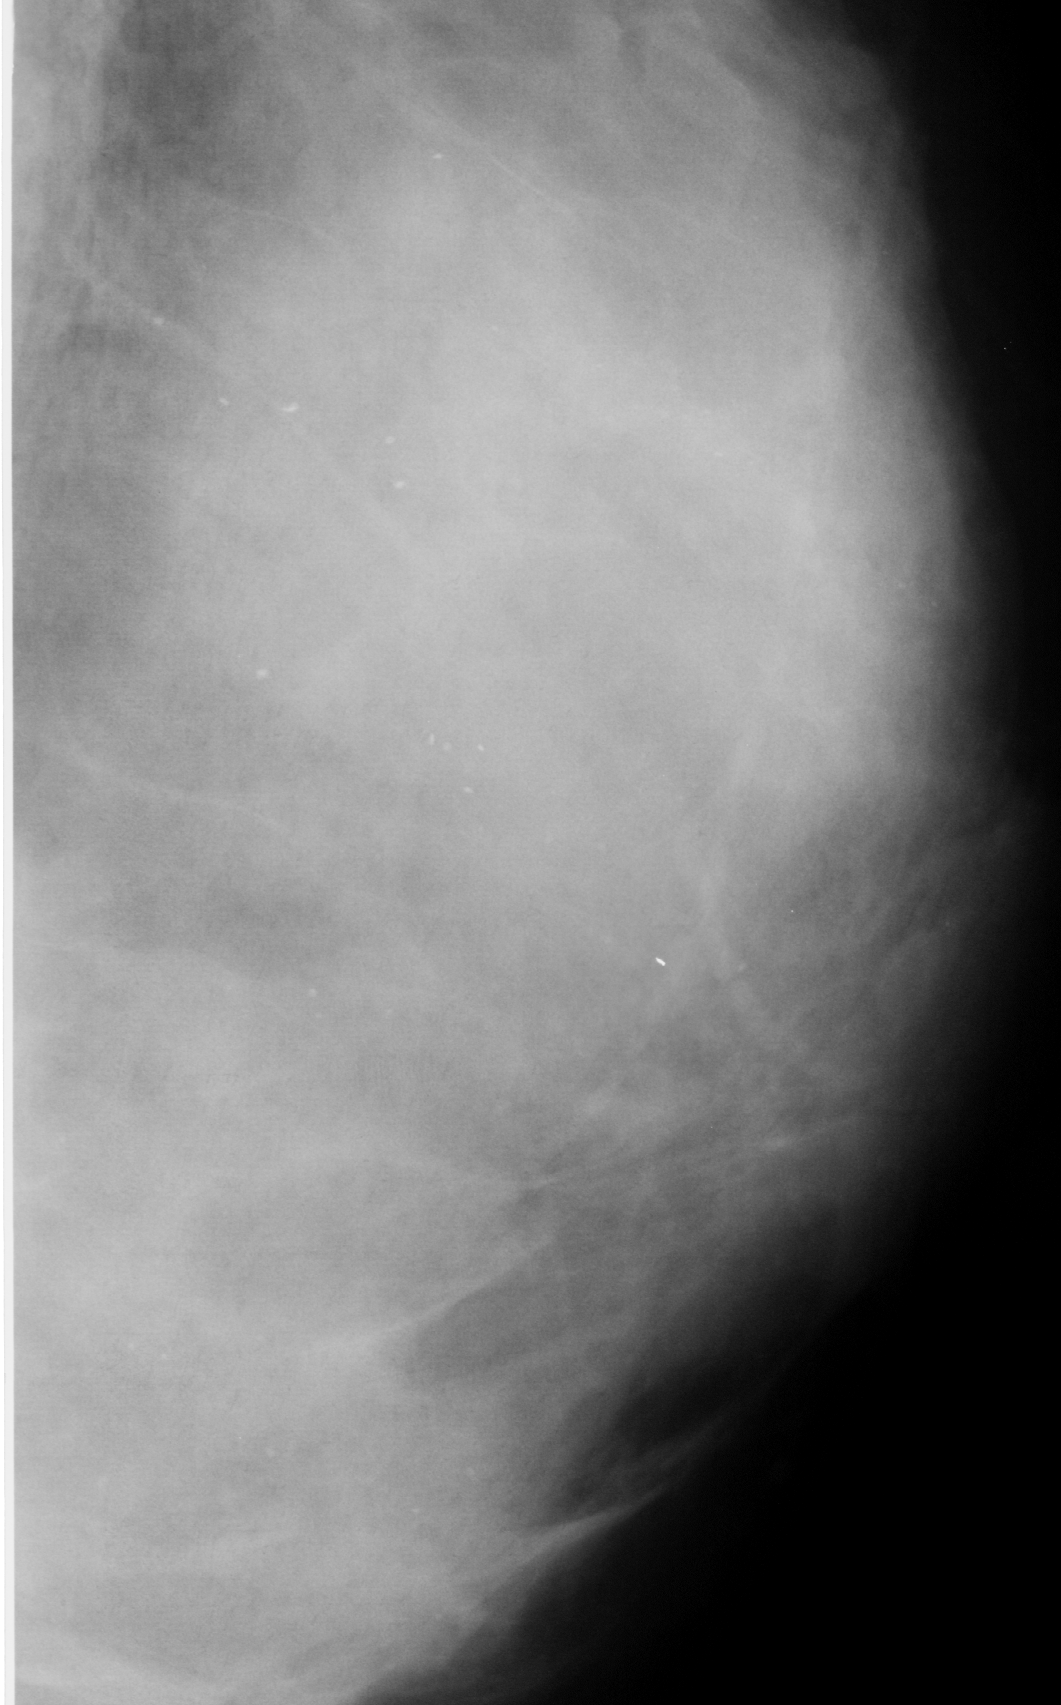
Cropped region of a digitized screen-film mammogram centred on a radiologist-marked abnormality, left breast, MLO view.
Calcifications, morphology punctate, distribution diffusely scattered; BI-RADS assessment category 2; subtlety rating 4 on a 1 (subtle) to 5 (obvious) scale; pathology (as recorded): benign.